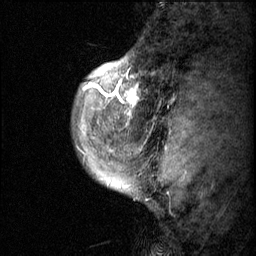
Breast MRI (dynamic contrast-enhanced), one sagittal slice; slice 9 of 60 in the series (ordered by position); dynamic contrast-enhanced series, image 2 of 3 at this slice position (ordered by acquisition); 1.5 T; TE 4.2 ms, TR 11.1 ms; 256 × 256 image matrix, field of view 180 × 180 mm. Patient: female, 50 years.
Annotated regions visible in this slice (semi-automatic segmentation, software-assisted and operator-edited):
- analysis volume of interest (the breast-tissue region the enhancement analysis was run in; not a lesion): bounding box <82,56,153,143> (left, top, right, bottom; pixels)
- tumour enhancement mask (voxels above the 70 % enhancement threshold inside the analysis volume of interest): <83,56,140,139>